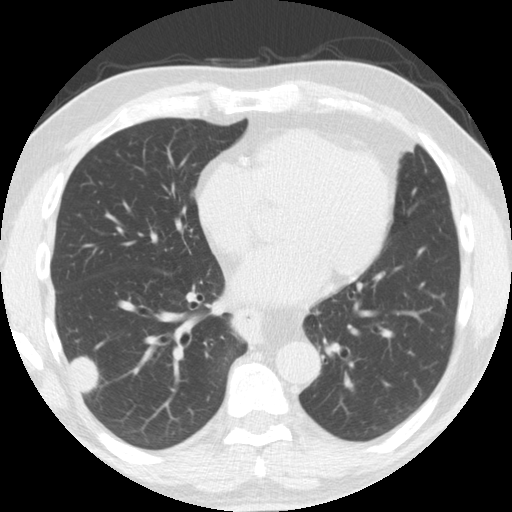
Low-dose screening chest CT, one axial slice. Position 72 of 174 along the scan axis. Reconstruction kernel STANDARD. Lung window (W 1500 / L -600 HU). 512 × 512 image matrix, field of view 341 × 341 mm.
Annotated regions visible in this slice (outlined manually by an expert reader):
- lesion 1 (tumor, lower lobe of right lung): bounding box (x1, y1, x2, y2) in pixels: (70, 356, 99, 394)